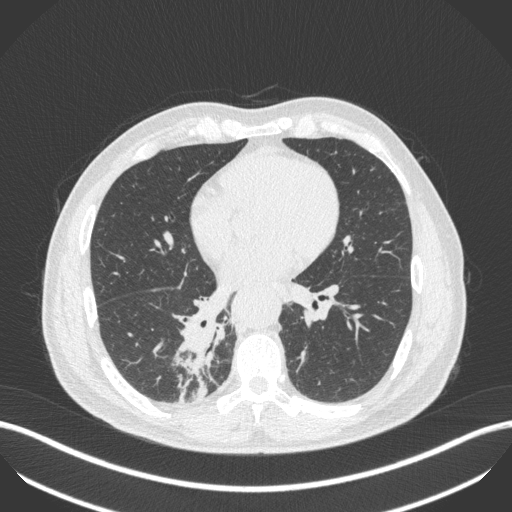
Chest CT, one axial slice; position 213 of 451 along the scan axis; lung window (W 1500 / L -600 HU); 1 mm slice thickness; 512 × 512 image matrix. Male patient, age 61 years. Case-level facts recorded for this patient, not image findings: clinical TNM (as recorded): T1 N0 M0; histopathological grade: G3.
Structures marked on this image (bounding box drawn by a radiologist):
- lung tumour (recorded histology: small cell carcinoma): bounding box <179,316,223,403> (left, top, right, bottom; pixels)